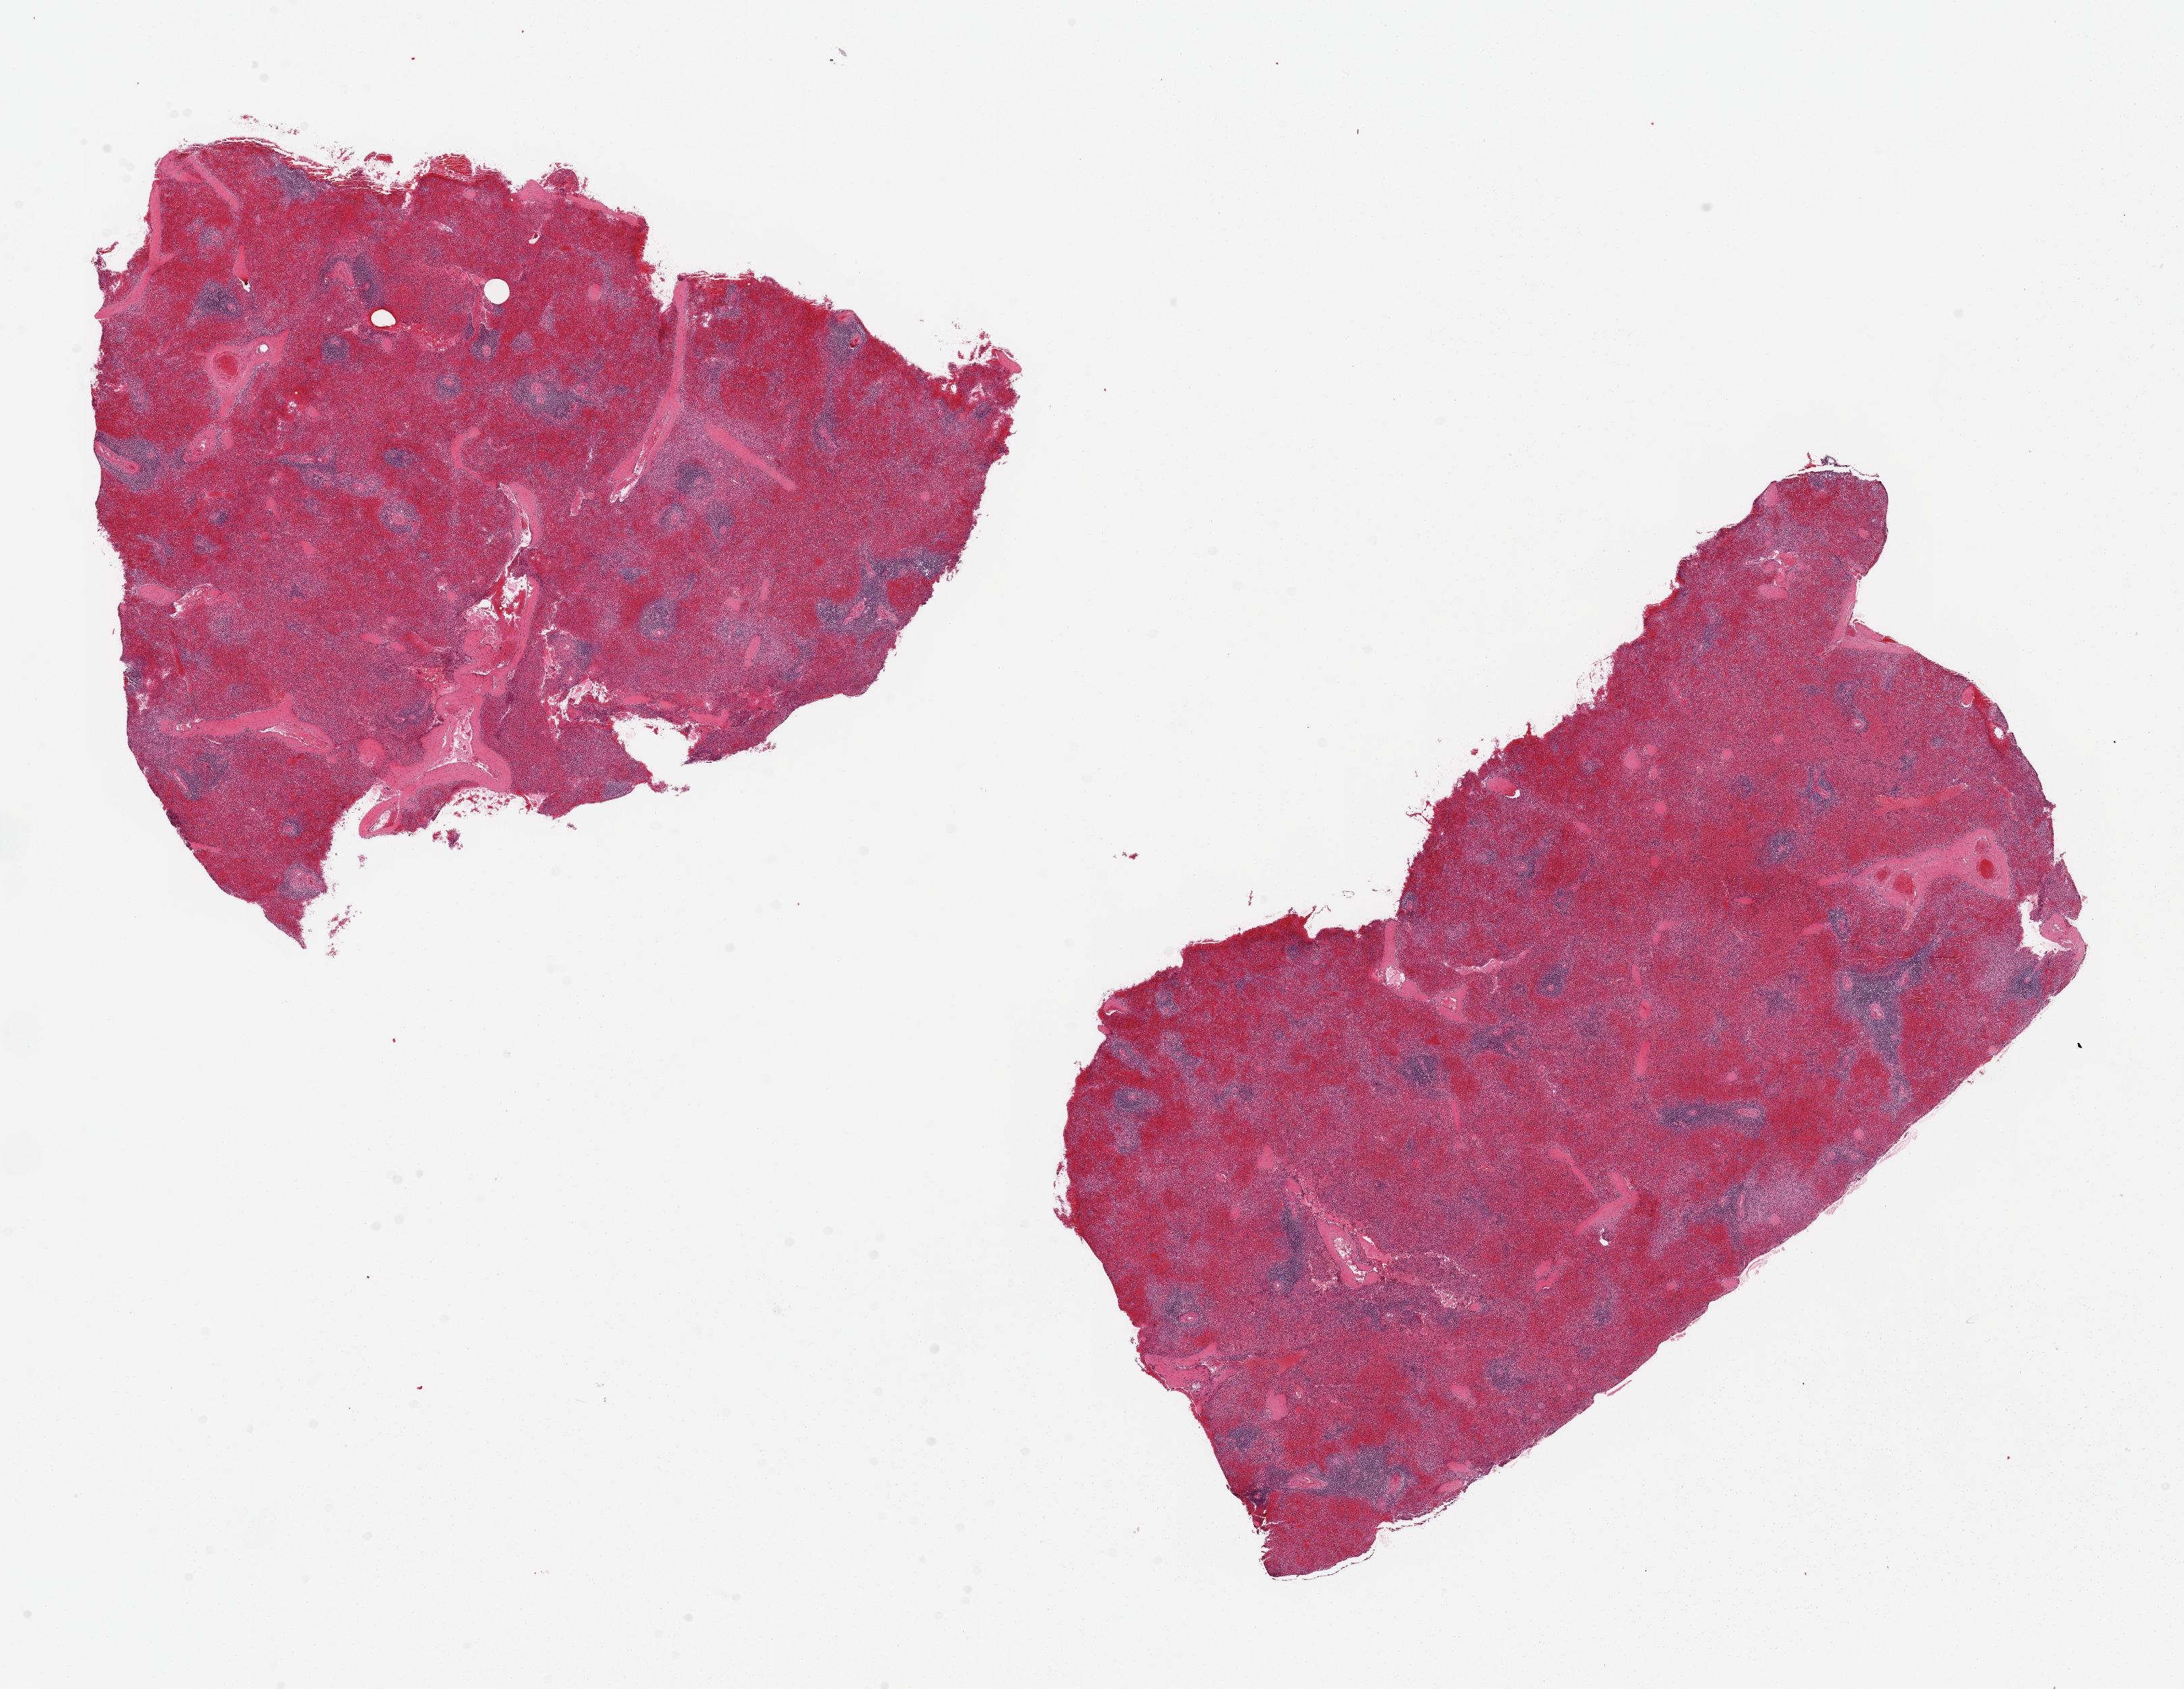
Whole-slide image, haematoxylin and eosin stain — shown as a low-resolution overview of the whole scanned area (about 25.6 x 19.8 mm); PAXgene-fixed paraffin-embedded (PFPE) section; sampled site (target tissue): spleen; tissue donor sample.
Pathologist's review note for this sample: 2 pieces, moderate congestion.